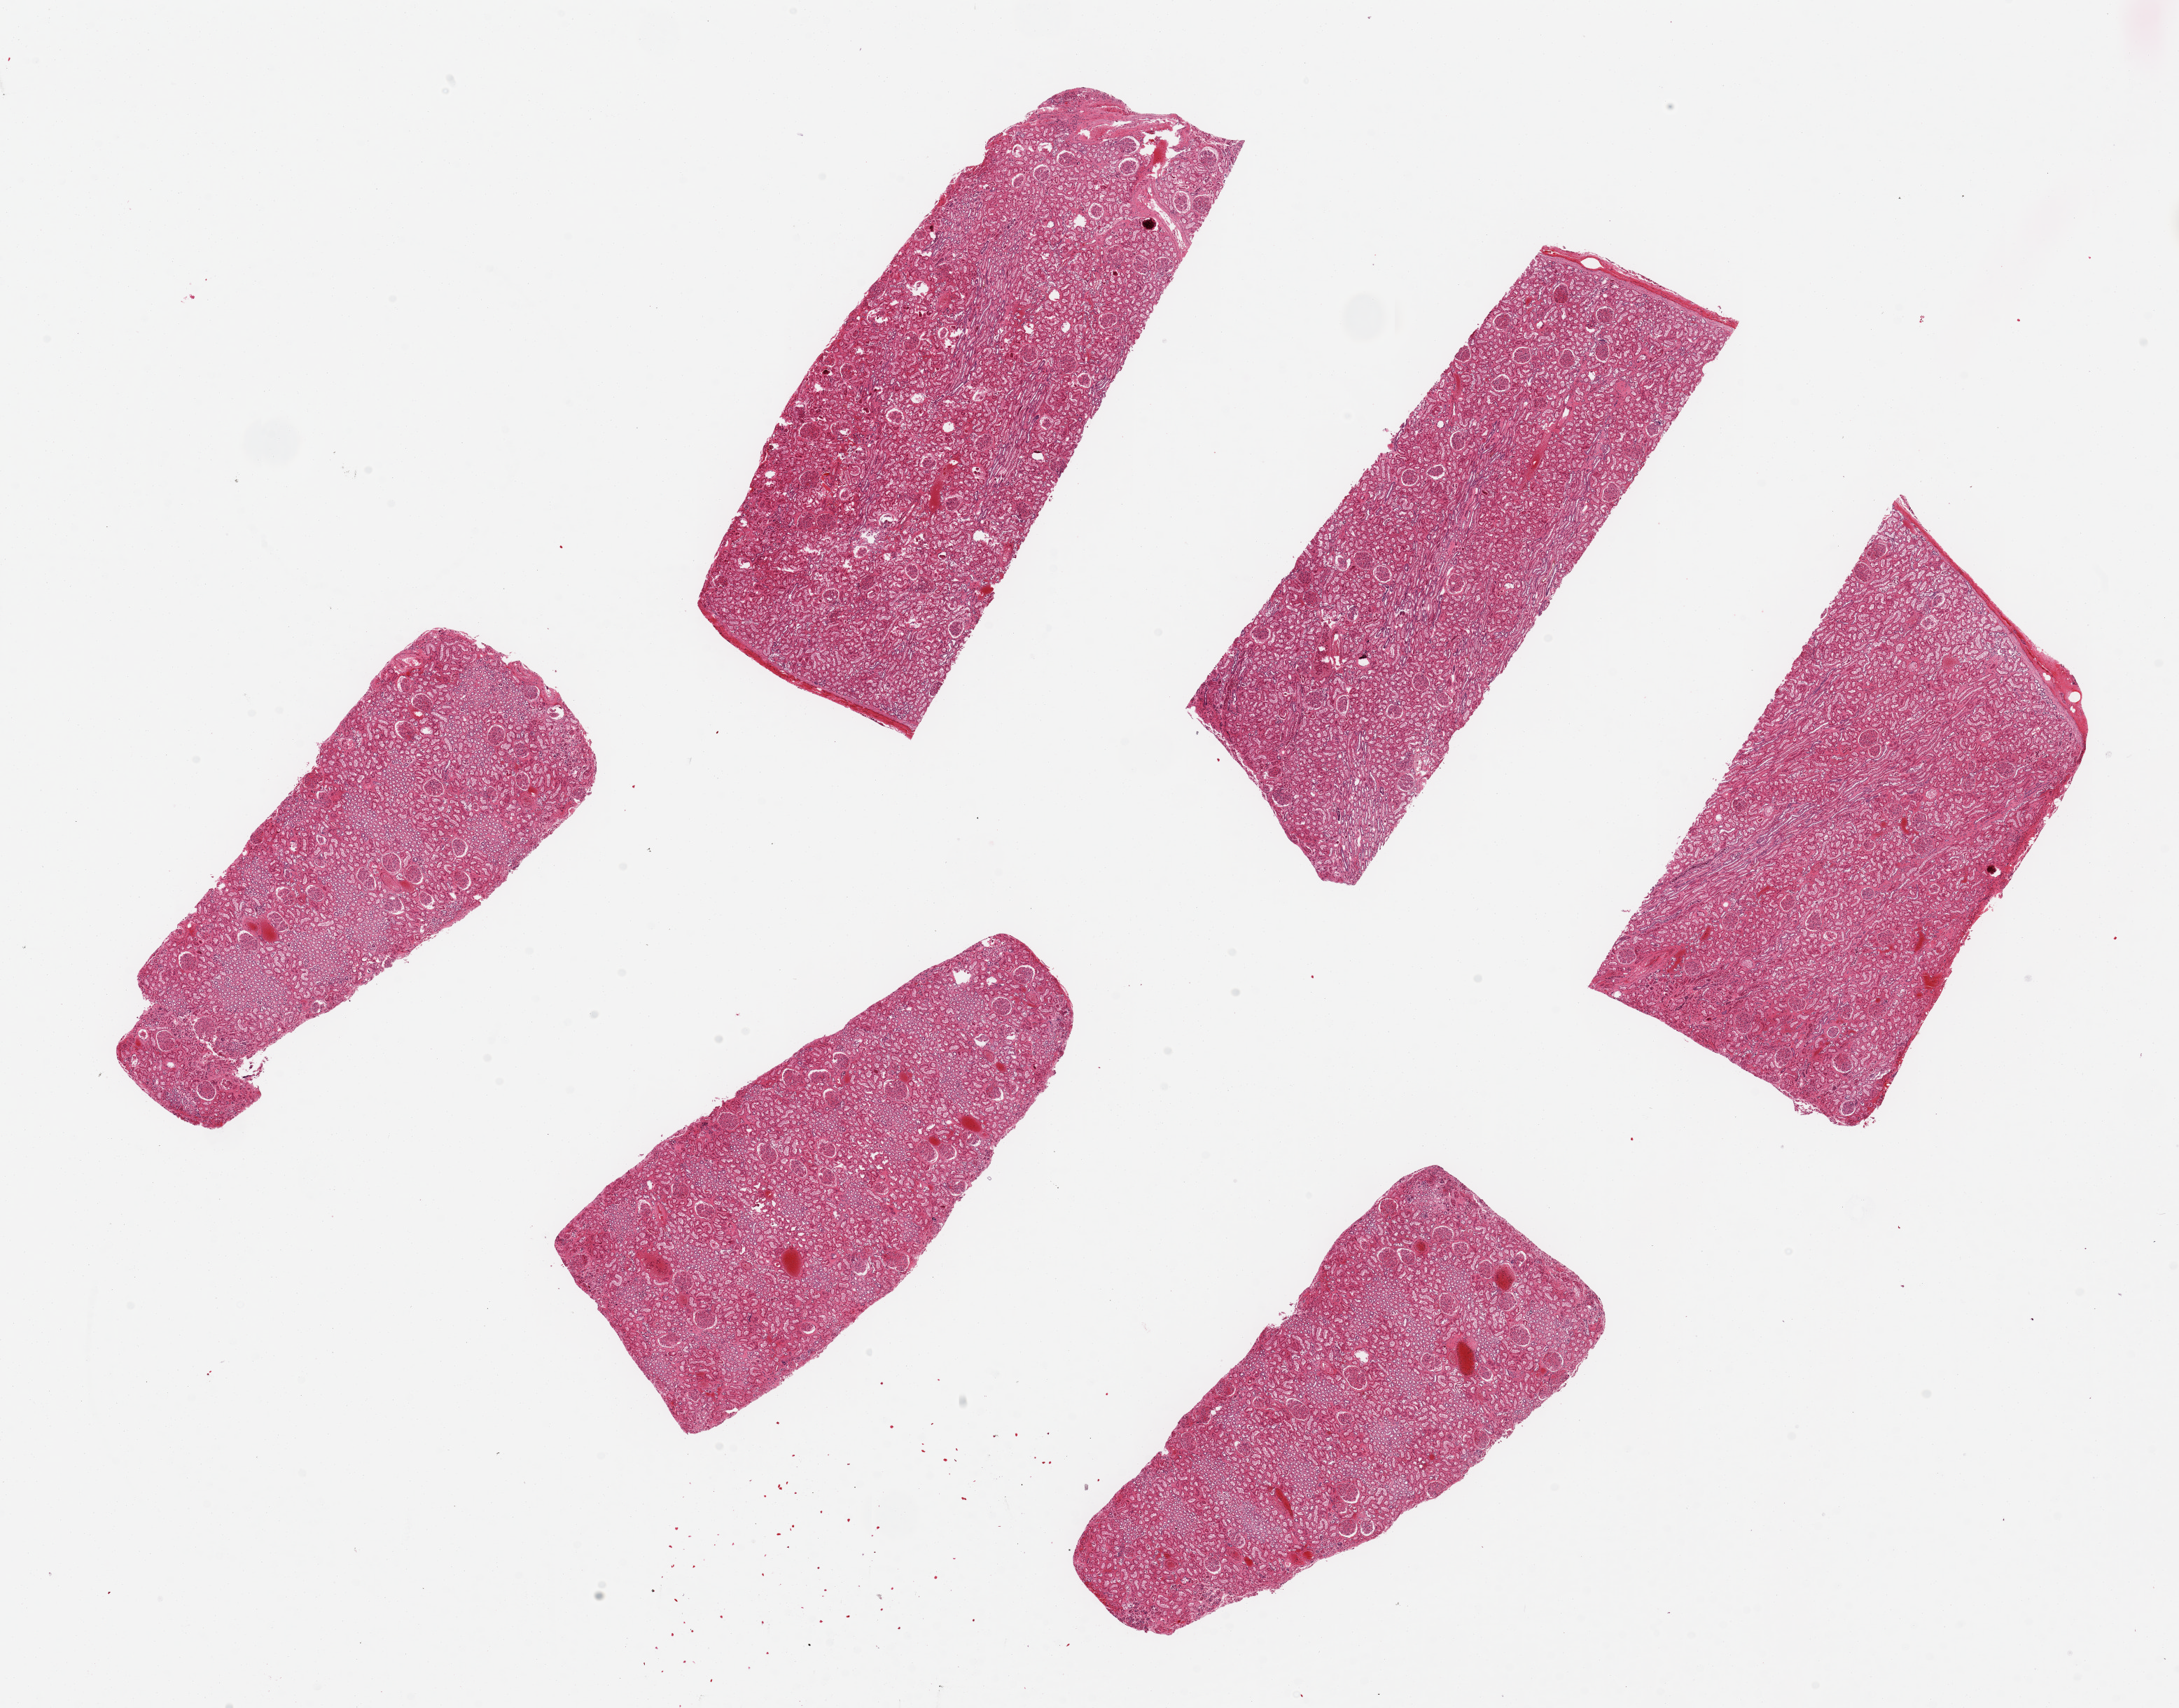
Whole-slide image, H&E stain — shown as a low-resolution overview of the whole scanned area (about 24.6 x 19.3 mm); PAXgene-fixed paraffin-embedded (PFPE) section; target tissue: renal cortex; tissue donor sample. Male donor.
Reviewer comment on this tissue sample: 6 pieces up to 8x3 mm; all cortex; good glomeruli.